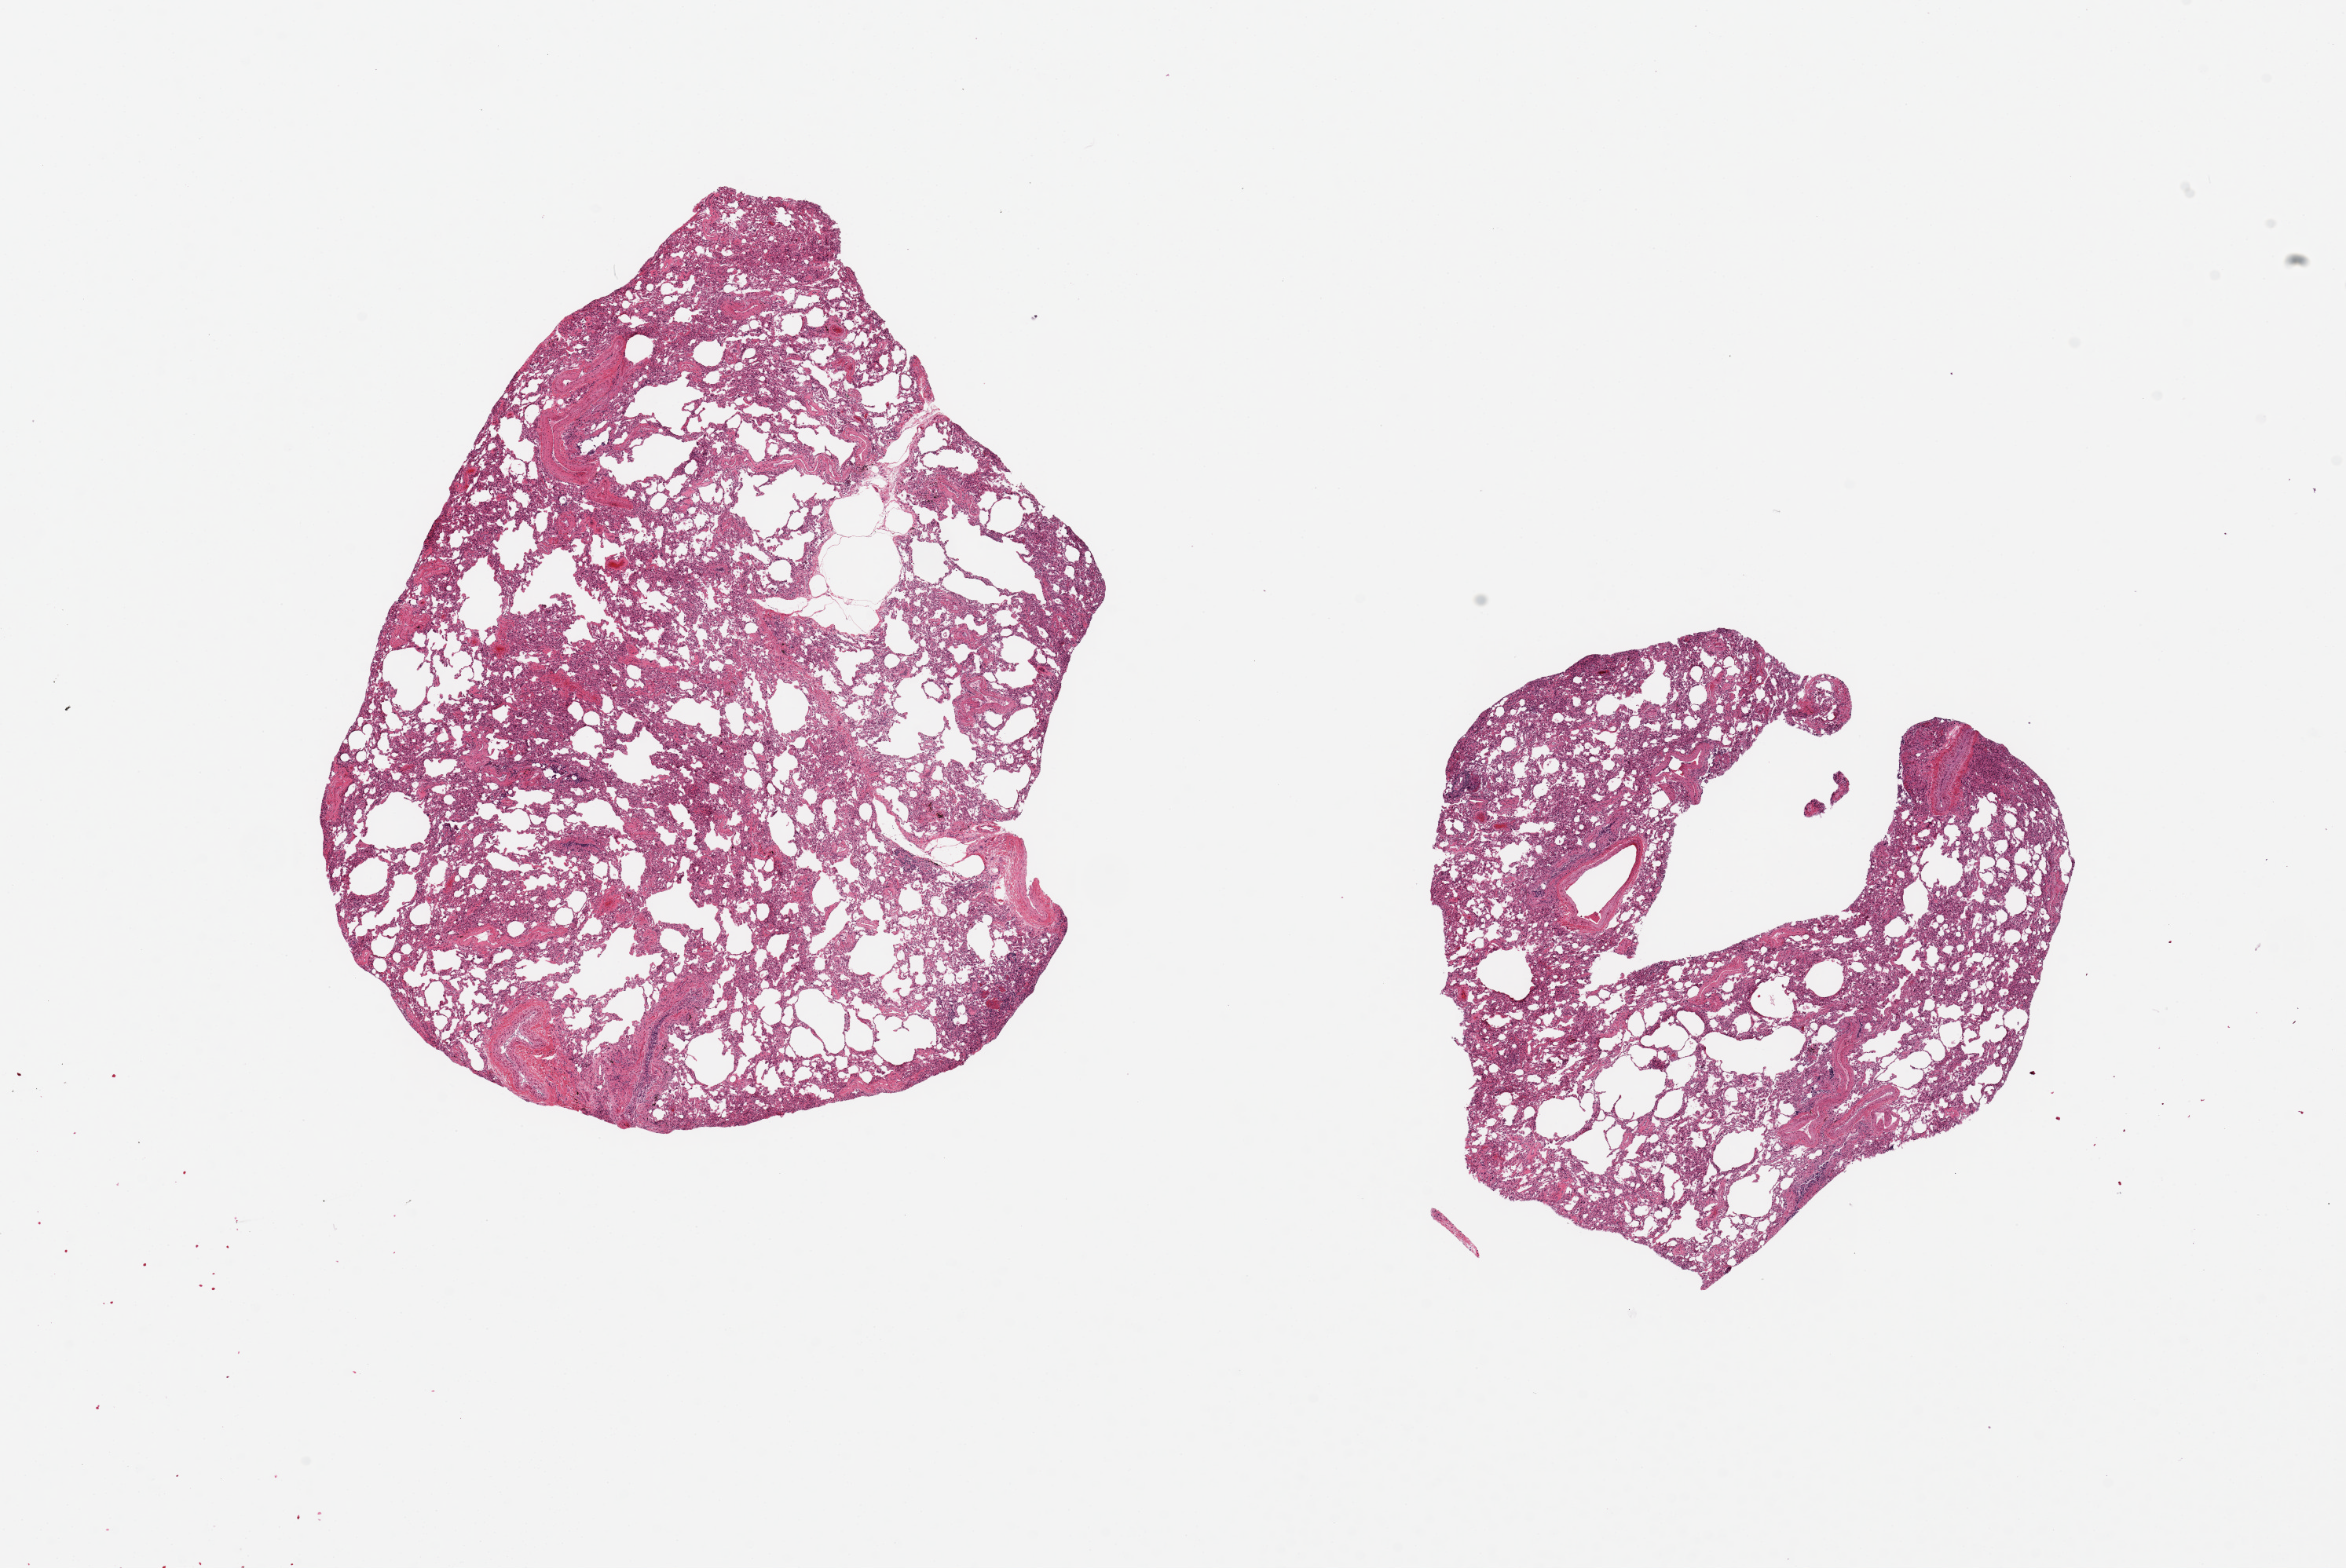
Digitized hematoxylin and eosin (H&E)-stained section, low-resolution overview of the scanned area, about 23.6 x 15.8 mm, PAXgene-fixed paraffin-embedded (PFPE) section, sampled site (target tissue): lung, tissue donor sample. Donor sex: male.
Review note (as recorded): 2 pieces, 8.5x7 & 5x6.3mm; small arteries thickened; heart failure cells.